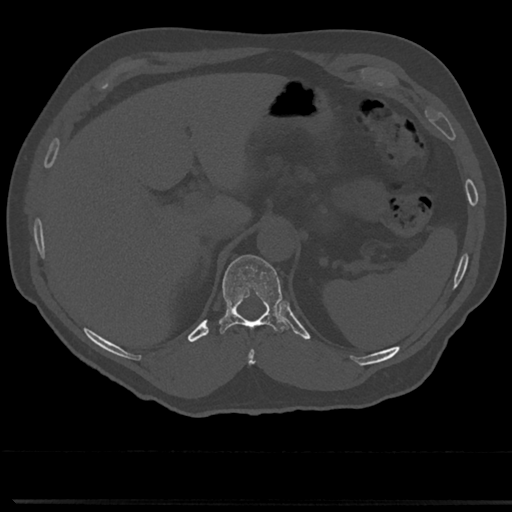
CT including the spine, one axial slice. Slice 208 of 817 in the series (ordered by position). 120 kVp. Bone window (W 1800 / L 400 HU). 0.5 mm slice thickness. 512 × 512 image matrix. Patient: male, 61 years. Case-level facts recorded for this patient, not image findings: primary cancer: prostate.
Outlined on this slice (semi-automatic segmentation, software-assisted and operator-edited):
- T10 vertebra: box from (x=246, y=339) to (x=256, y=366) px
- T11 vertebra: (x=214, y=255)–(x=290, y=335)